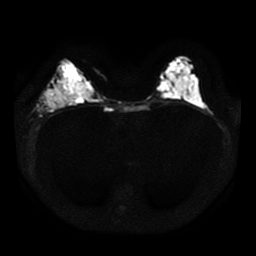
Breast MRI, one axial slice; slice 18 of 41 in the series (ordered by position); diffusion-weighted series; image 2 of 4 stored at this slice position (different b-values; order by instance number); 1.5 T; 5 mm slice thickness; 256 × 256 image matrix, field of view 330 × 330 mm. Female patient.
Annotated regions visible in this slice (outlined manually by an expert reader):
- tumour on diffusion-weighted imaging: box from (x=45, y=89) to (x=76, y=109) px